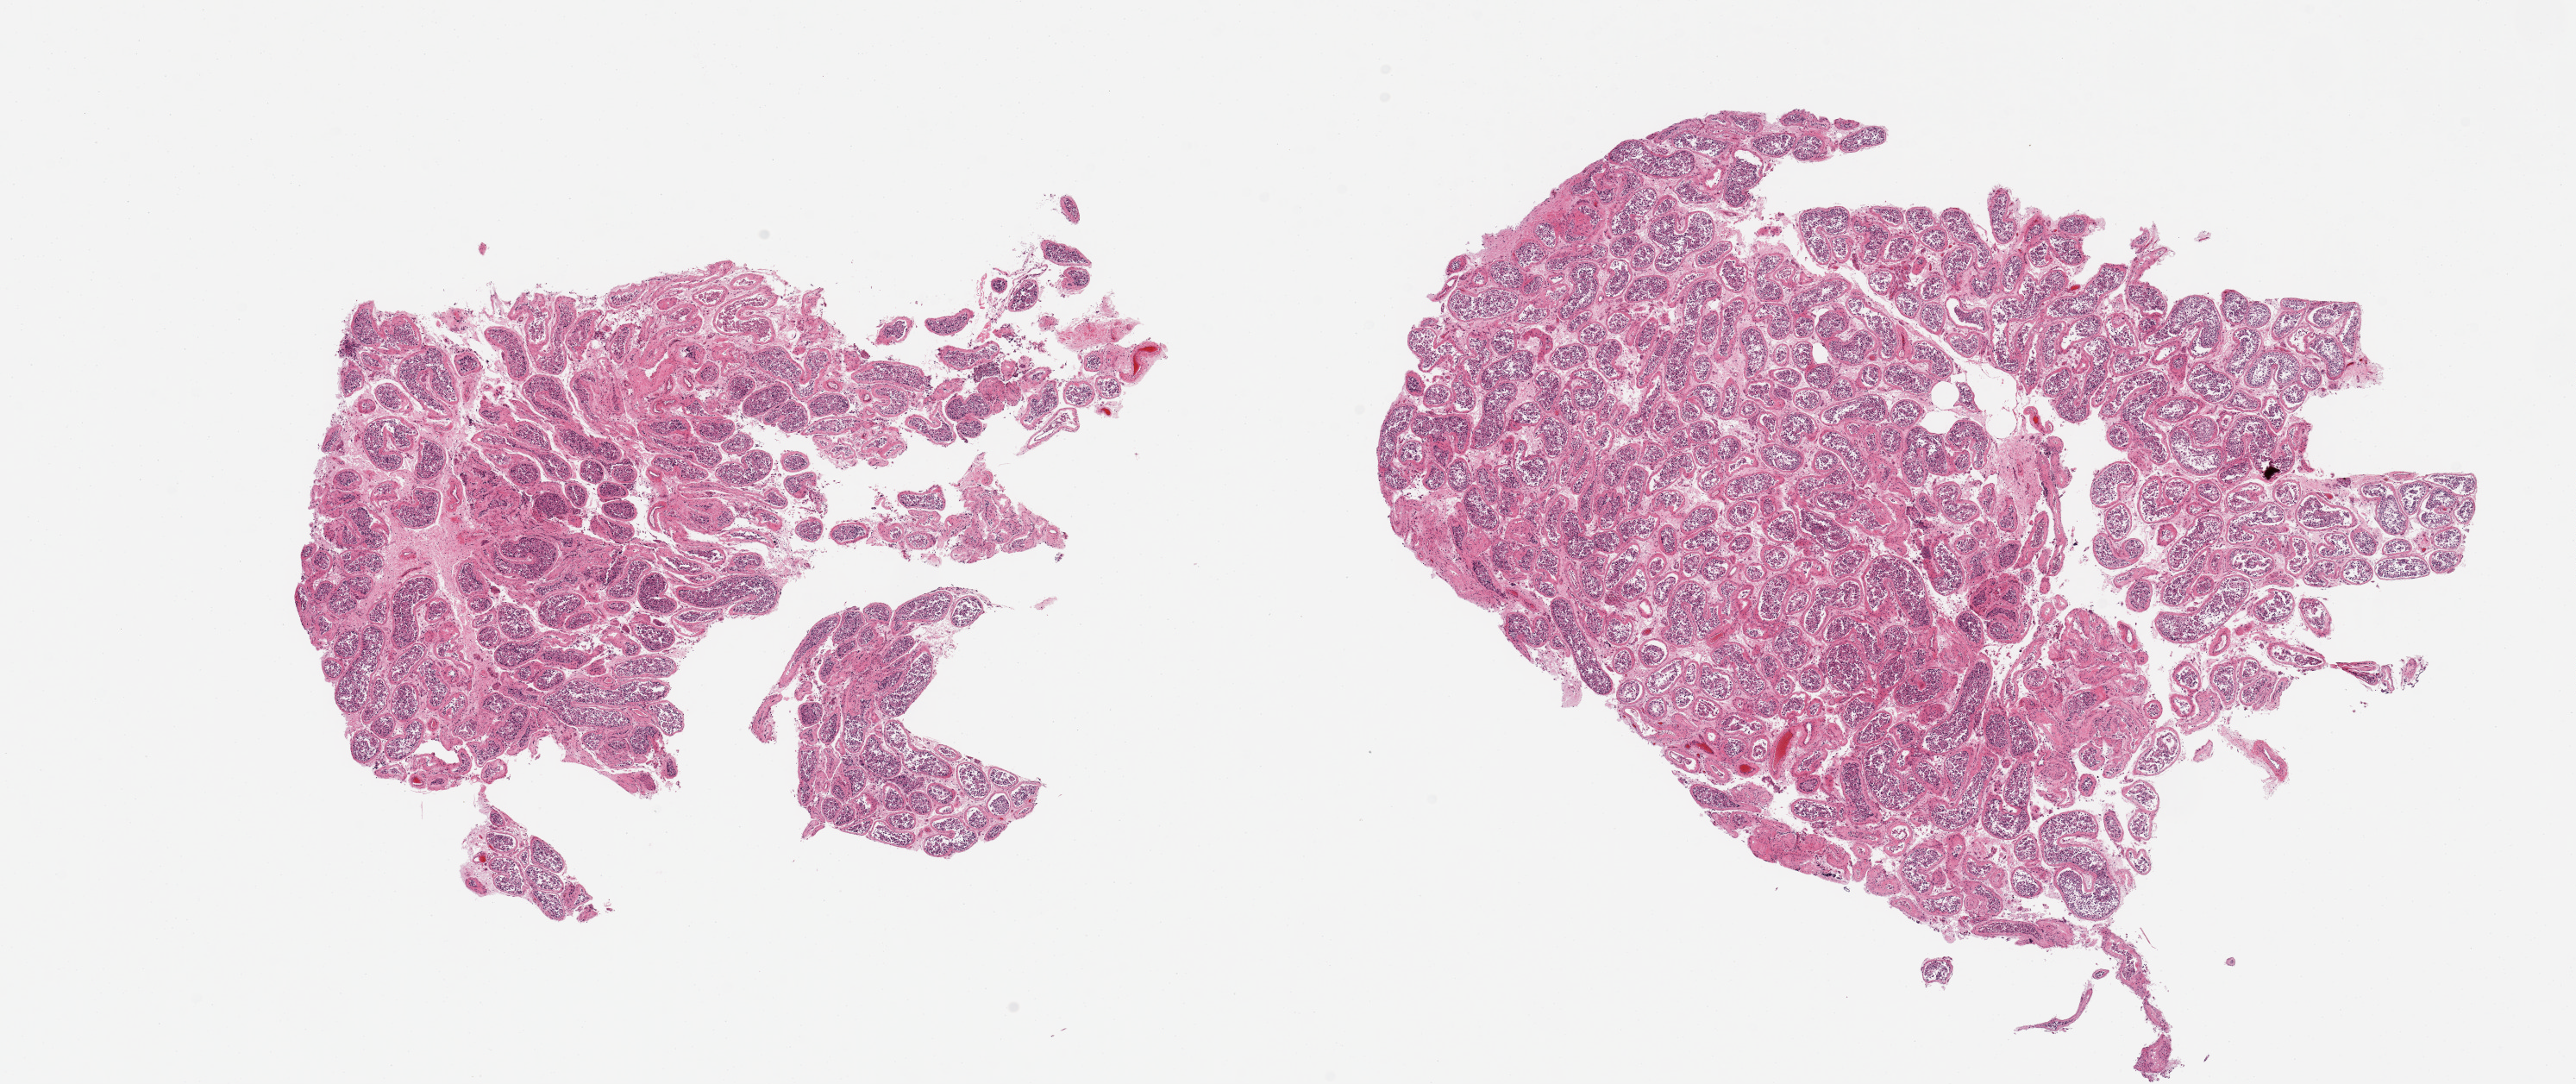
Whole-slide image, H&E stain — low-resolution overview of the scanned area, about 23.6 x 9.9 mm, PAXgene-fixed, paraffin-embedded tissue, section of testis (target tissue), donor tissue sample.
Reviewer comment on this tissue sample: 2 pieces, spermatogenesis appears reduced.